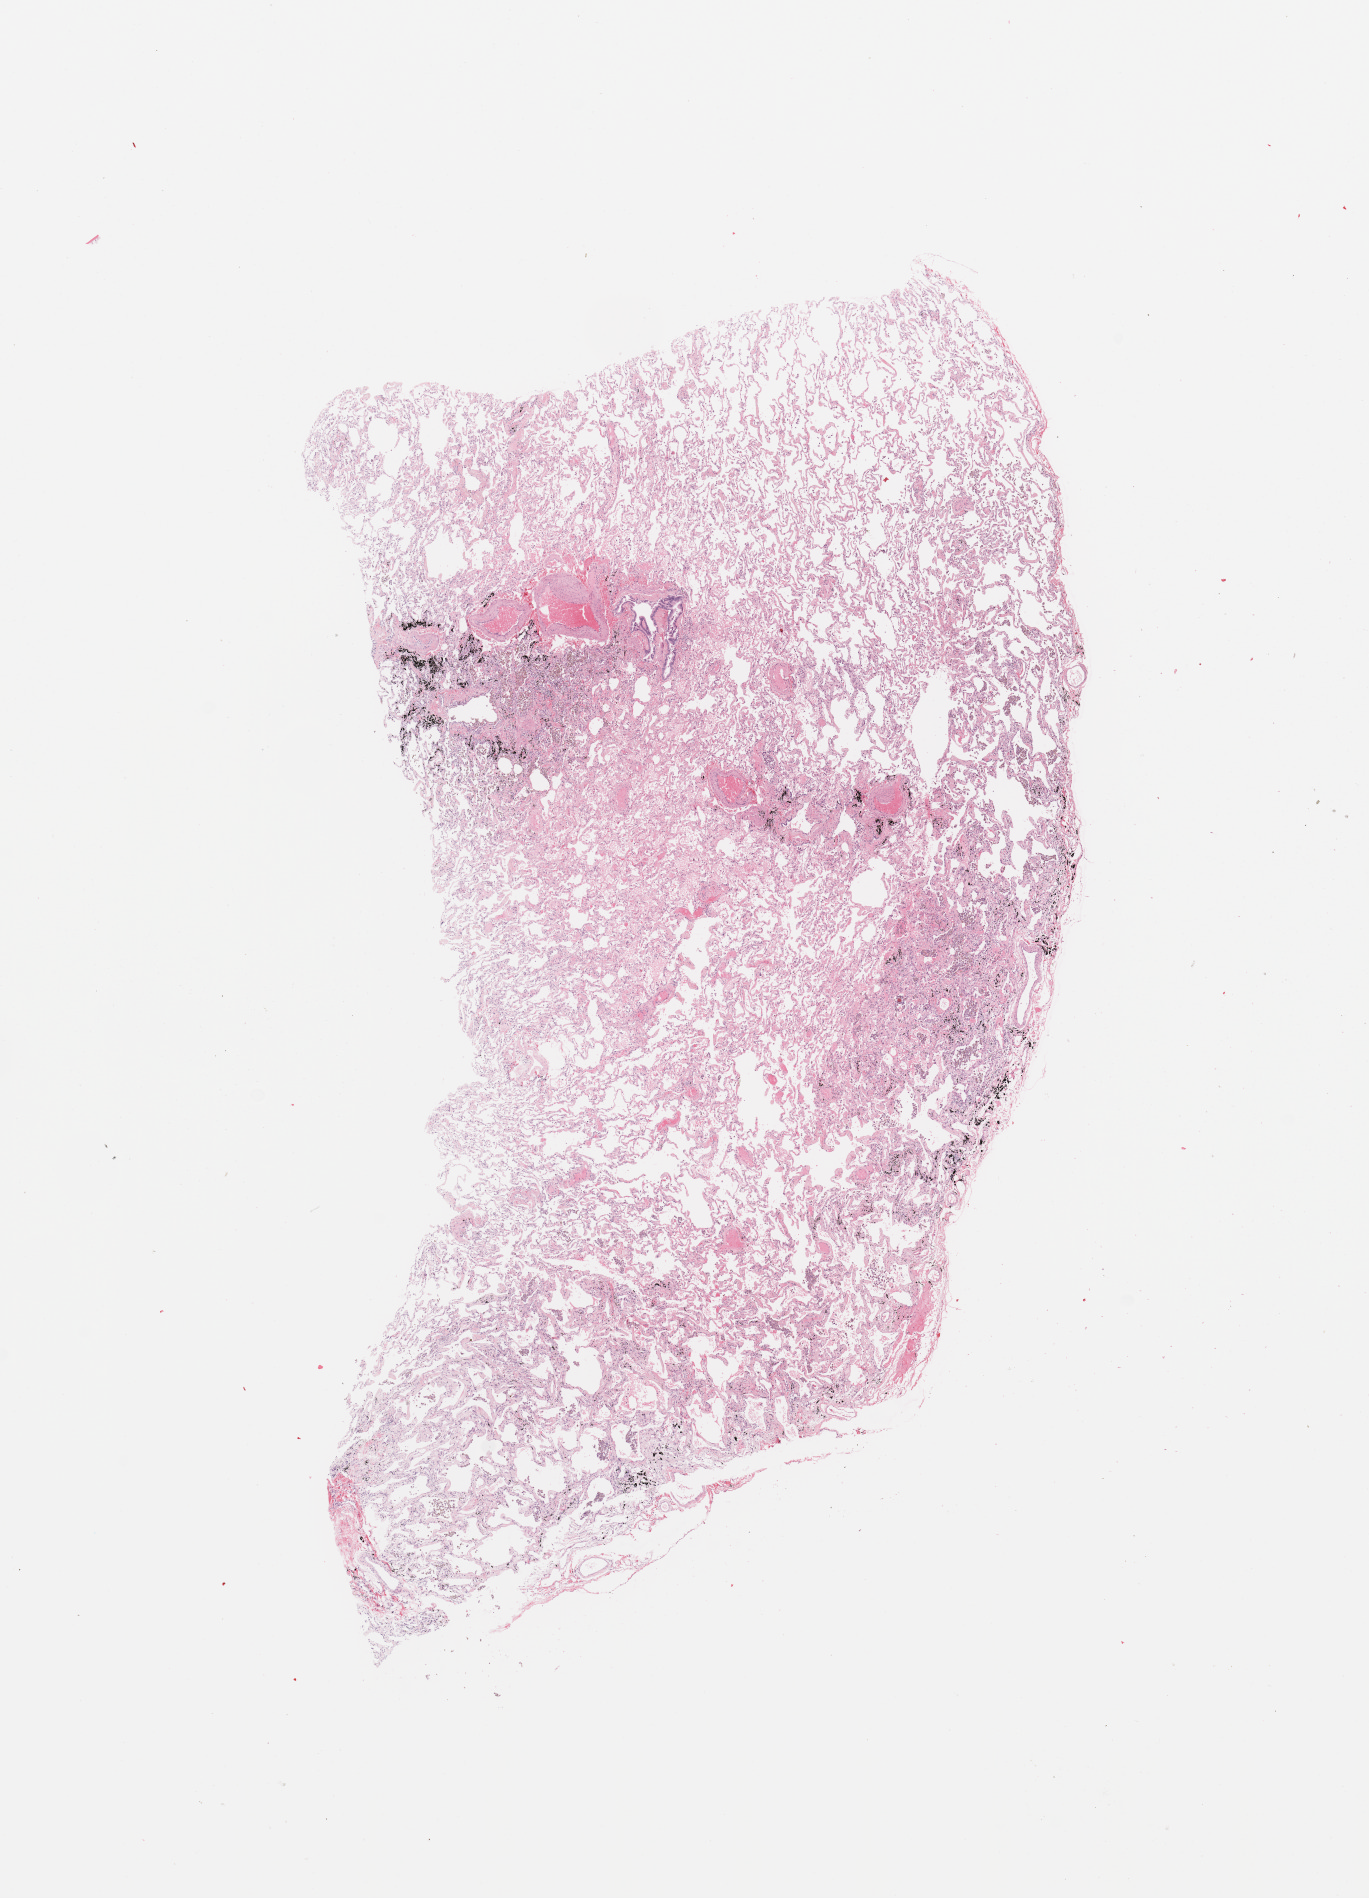
H&E whole-slide image, shown as a low-resolution overview of the whole scanned area (about 10.8 x 15.0 mm, slide scanned at 20x), normal (non-tumour) tissue sample, sampled site: lung. Male, 65 y/o.
This section: normal (non-tumour) tissue from the same patient. Patient diagnosis: Squamous cell carcinoma, NOS.